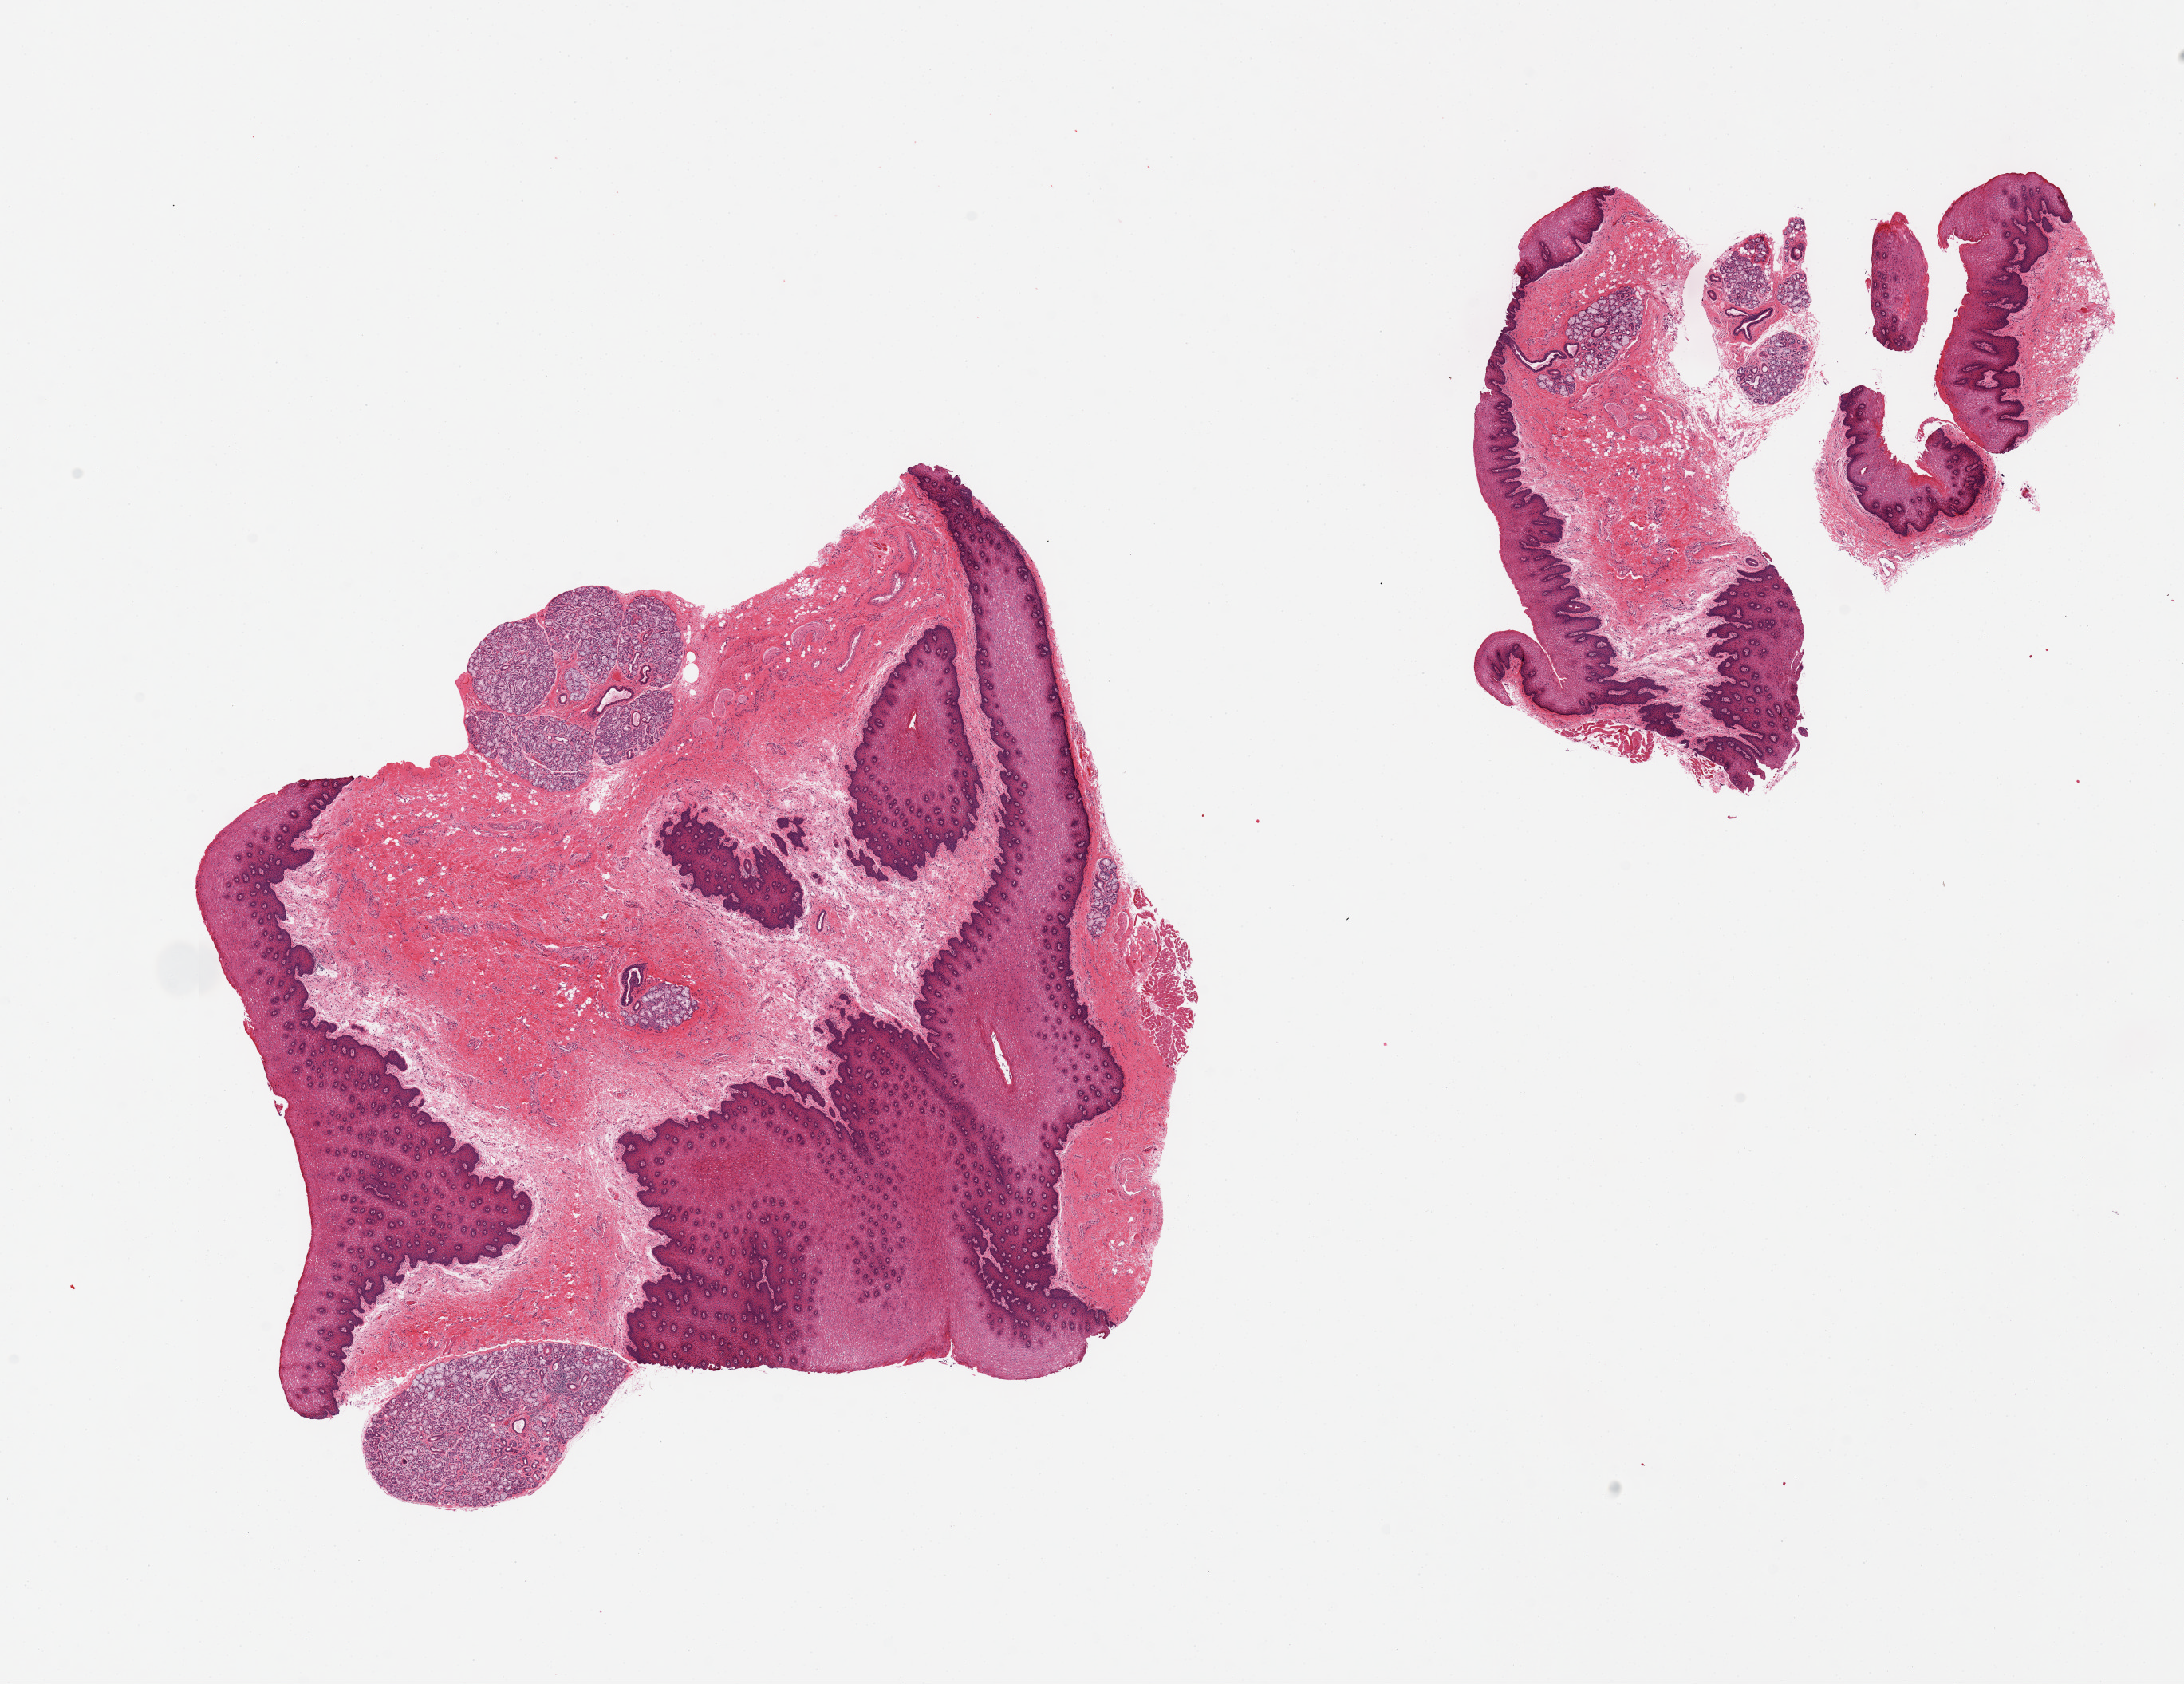
Haematoxylin and eosin whole-slide image, brightfield — a low-resolution overview of the entire scanned area, about 21.7 x 16.7 mm (slide scanned at 20x); PAXgene-fixed paraffin-embedded (PFPE) section; sampled site (target tissue): minor salivary gland; tissue donor sample.
- pathologist's review note for this sample: 2 pieces, ~10% is salivary gland elements with mild chronic inflammation, the remainder is lip, stroma, skeletal muscle